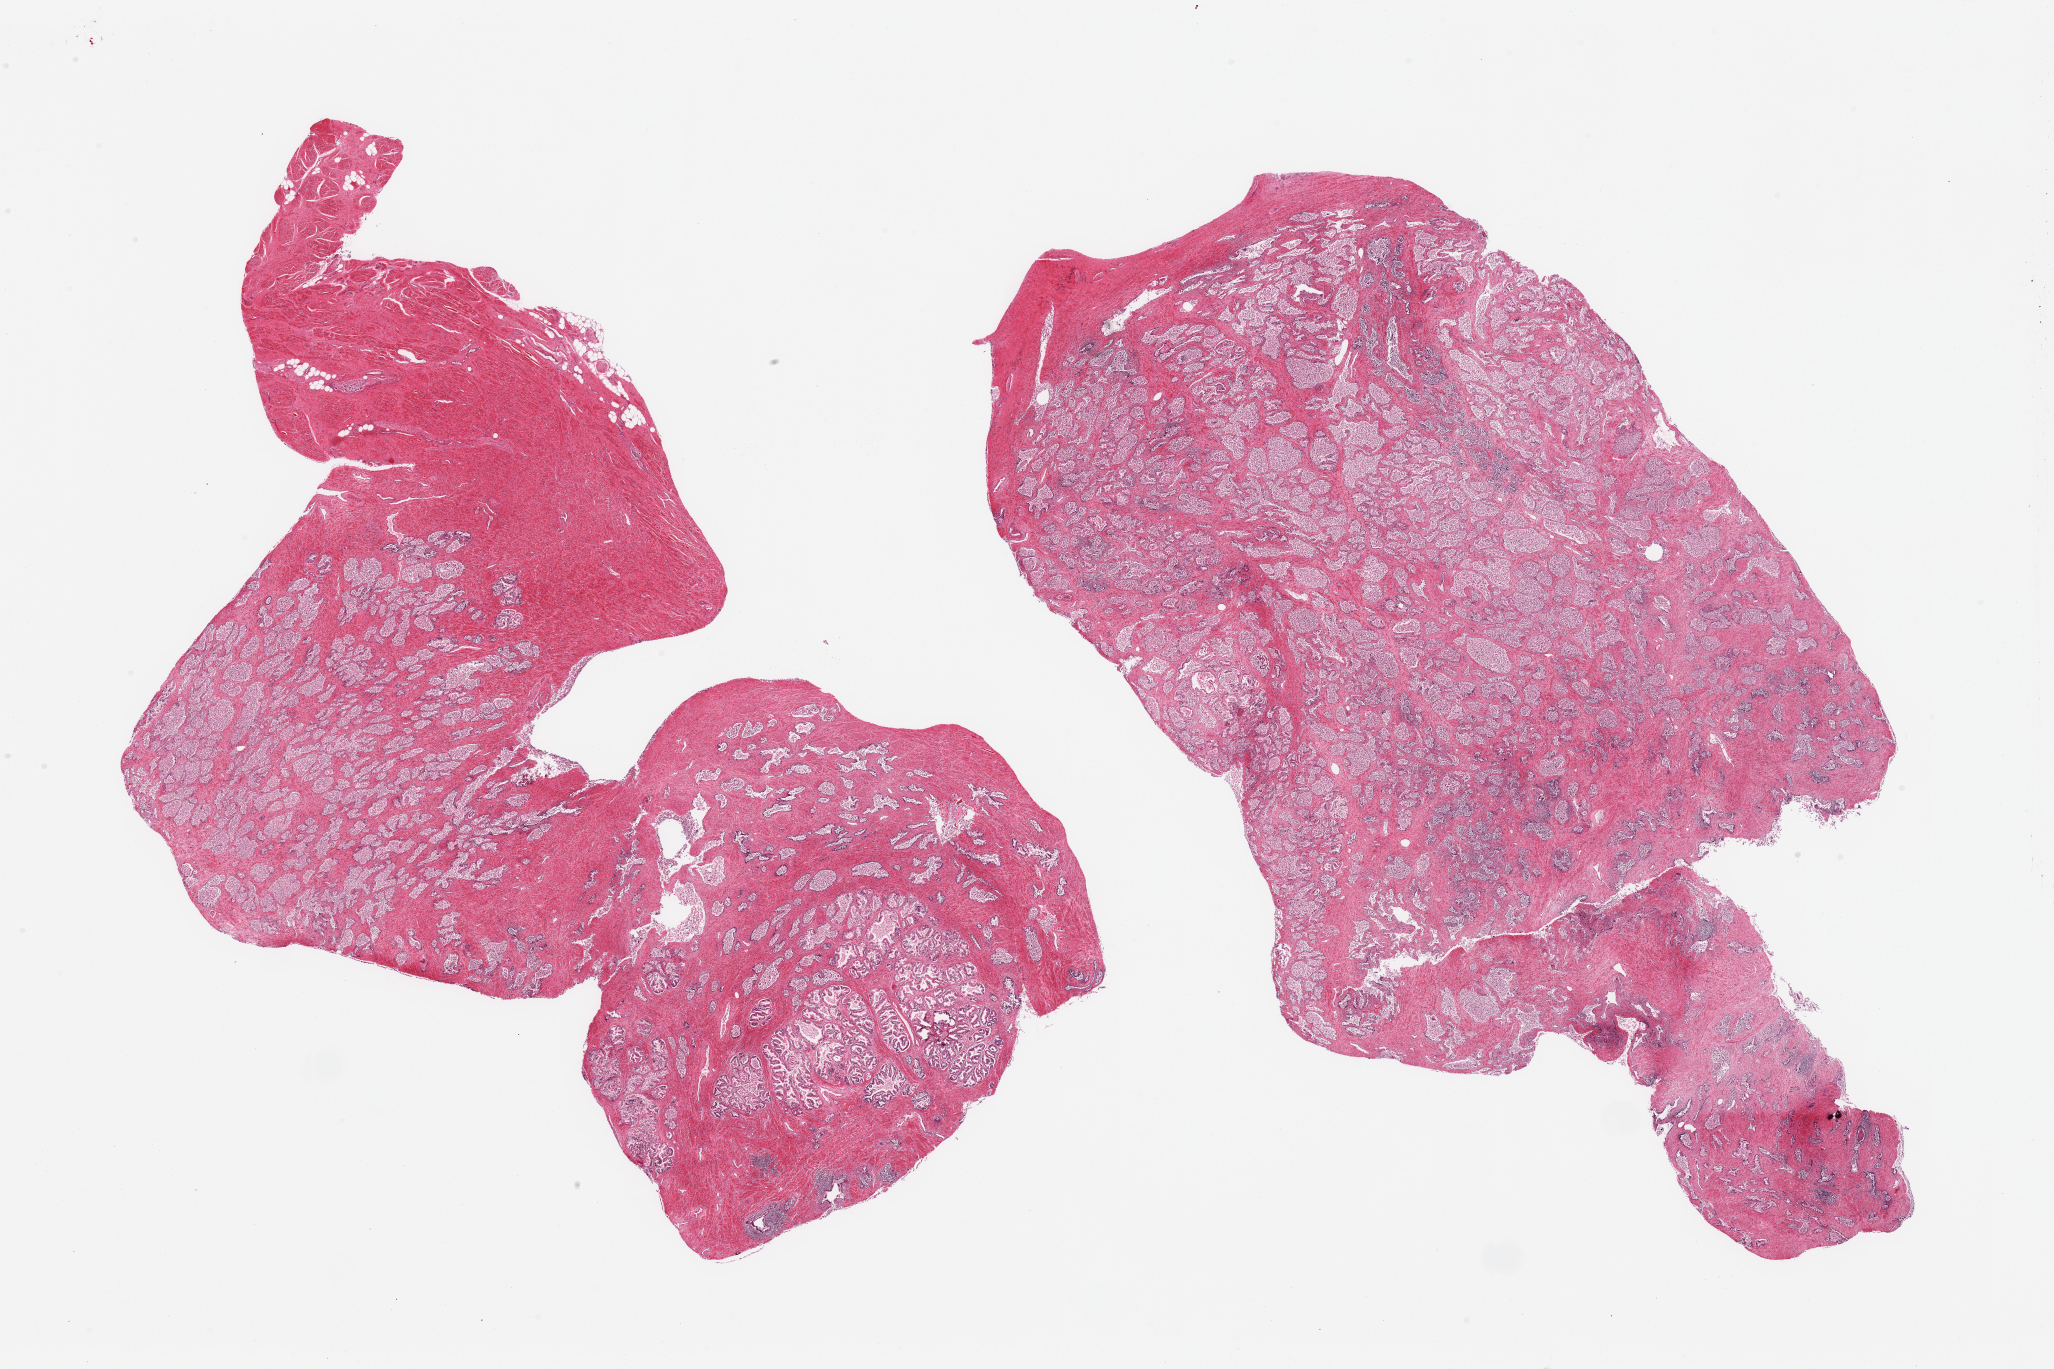
Digitized haematoxylin and eosin-stained section, brightfield, whole scanned area (about 32.5 x 21.7 mm) shown as a low-resolution overview. PAXgene-fixed, paraffin-embedded tissue. Target tissue: prostate. Tissue donor sample. Donor sex: male.
* pathologist's review note for this sample: 2 pieces; glandular hyperplasia and generalized sloughing of glandular epithelium; periglandular lymphocytic infiltrates; fibromuscular stroma; focal calcification